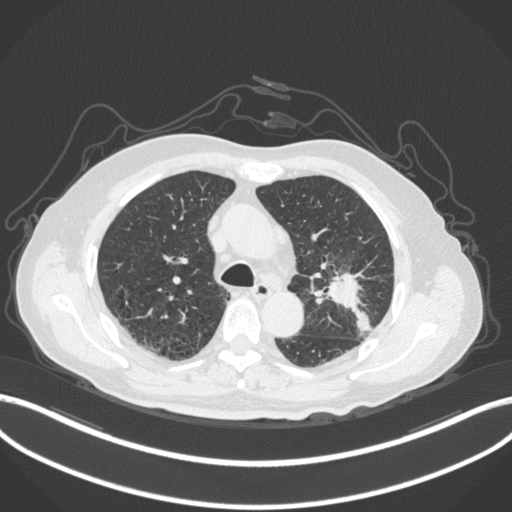
Chest CT, one axial slice. Slice 196 of 331 in the series (ordered by position). 120 kVp. Lung window (W 1500 / L -600 HU). 1 mm slice thickness. 512 × 512 image matrix, field of view 400 × 400 mm. Patient: male, 79 years. Case-level facts recorded for this patient, not image findings: clinical TNM (as recorded): T2a N1 M1; histopathological grade: G3.
Structures marked on this image (rectangle marked by the reading radiologist):
- lung tumour (recorded histology: adenocarcinoma): bounding box <323,271,374,337> (left, top, right, bottom; pixels)